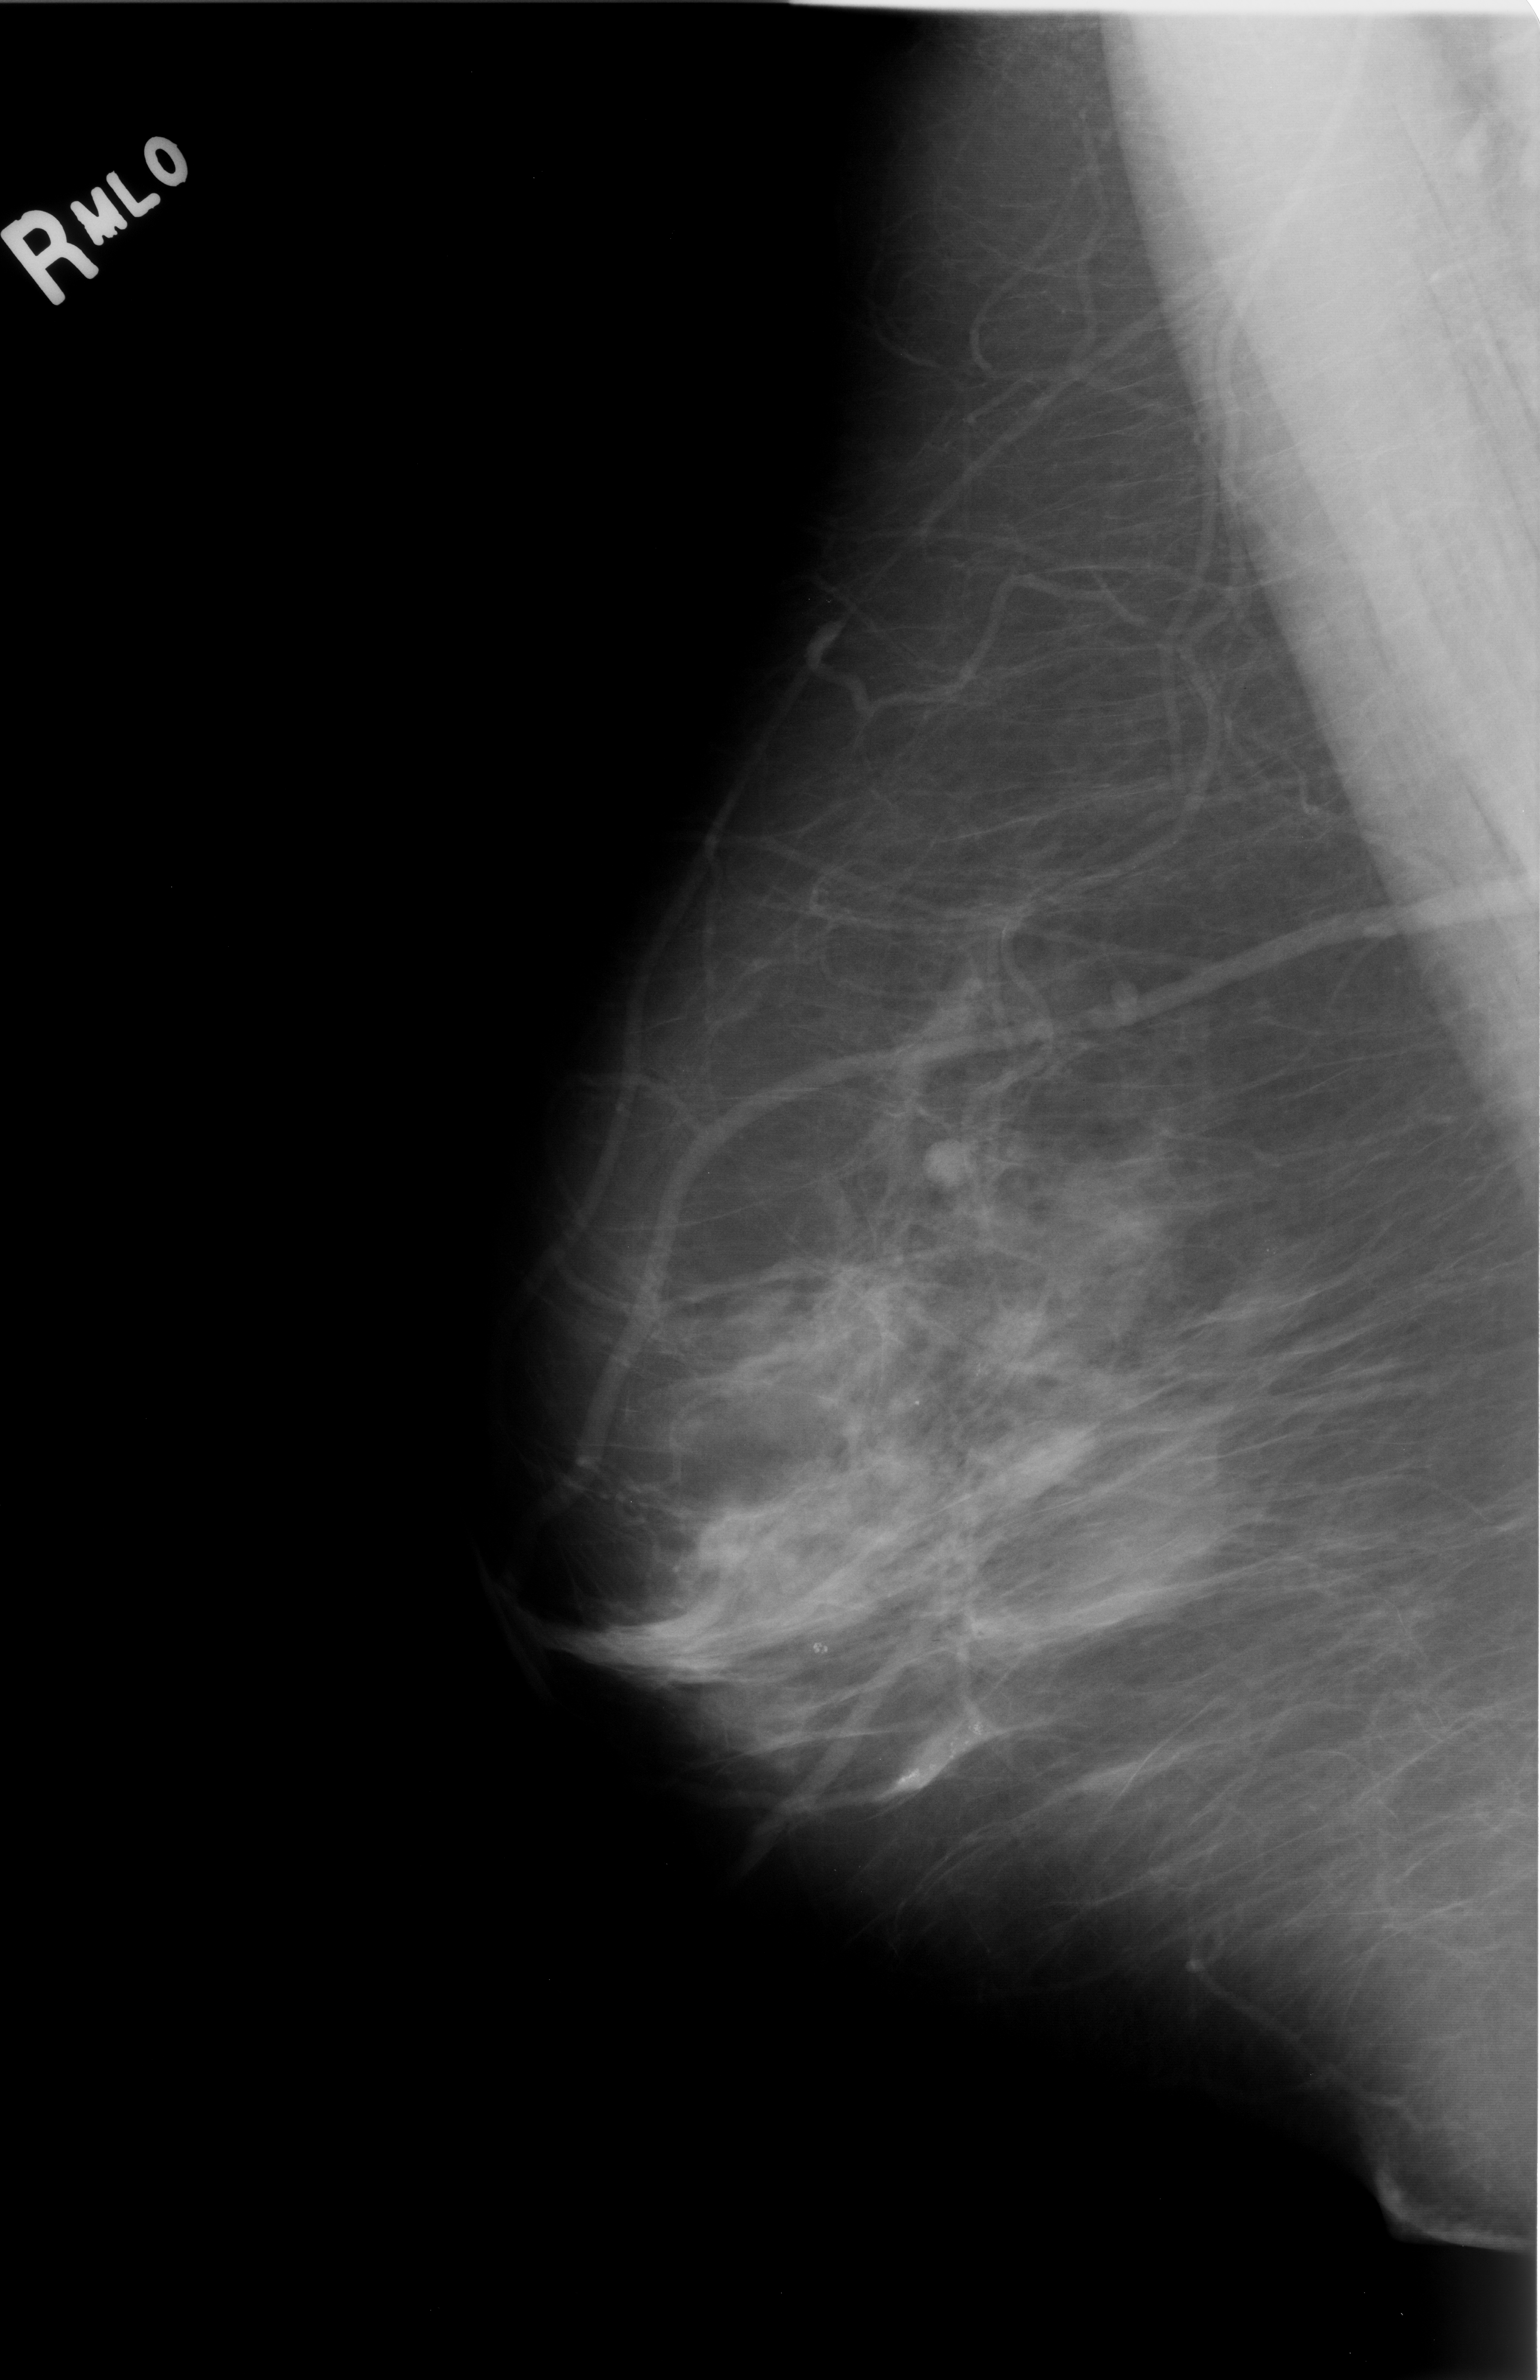
Mammogram (digitized film); right breast; MLO view; BI-RADS breast density category 2 (scale 1–4).
- Finding: mass, shape round, margins circumscribed; BI-RADS assessment category 2; benign; no additional work-up was recommended (benign without callback).